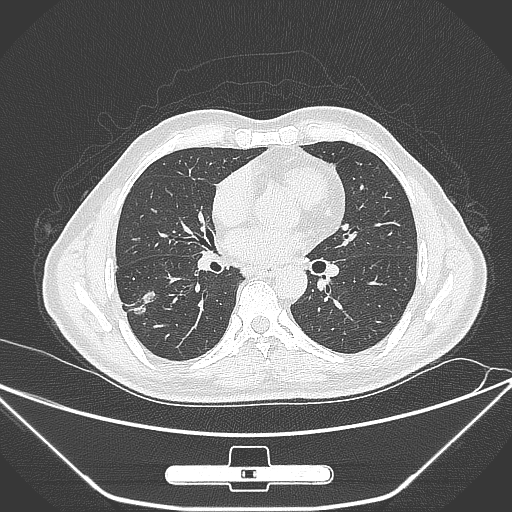
Chest CT, one axial slice; slice 141 of 310 in the series (ordered by position); 120 kVp; lung window (W 1500 / L -600 HU); 1 mm slice thickness; 512 × 512 image matrix, field of view 398 × 398 mm. Male patient, age 71 years. Case-level facts recorded for this patient, not image findings: clinical TNM (as recorded): T1c N0 M0.
Structures marked on this image (bounding box drawn by a radiologist):
- lung tumour (recorded histology: adenocarcinoma): bounding box <122,283,165,326> (left, top, right, bottom; pixels)